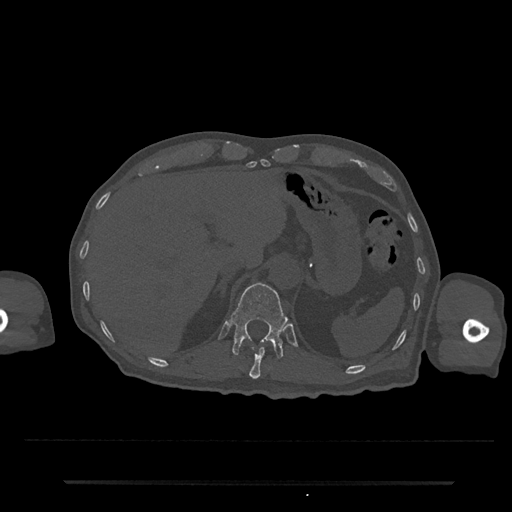
CT including the spine, one axial slice; position 217 of 797 along the scan axis; reconstruction kernel Br40s/3; bone window (W 1800 / L 400 HU); 512 × 512 image matrix, field of view 427 × 427 mm. Patient: male, 74 years. Case-level facts recorded for this patient, not image findings: primary cancer: prostate.
Structures marked on this image (semi-automatic segmentation, software-assisted and operator-edited):
- T11 vertebra: bounding box <243,343,273,379> (left, top, right, bottom; pixels)
- T12 vertebra: <231,283,288,359>